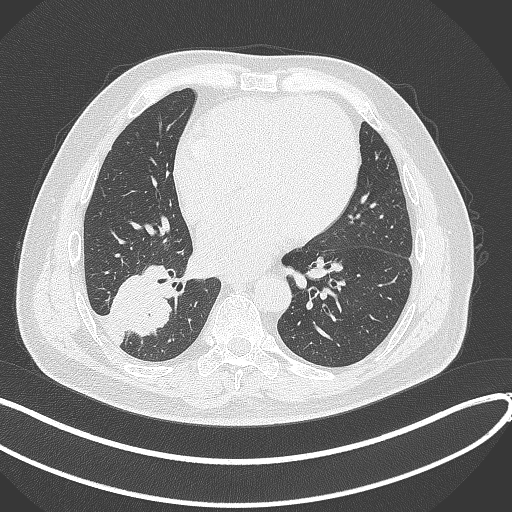
Chest CT, one axial slice. Position 146 of 360 along the scan axis. 120 kVp. Lung window (W 1500 / L -600 HU). 1 mm slice thickness. 512 × 512 image matrix. Male patient, age 59 years.
Outlined on this slice (rectangle marked by the reading radiologist):
- lung tumour (recorded histology: adenocarcinoma): bounding box [x1, y1, x2, y2] px = [111, 260, 178, 341]